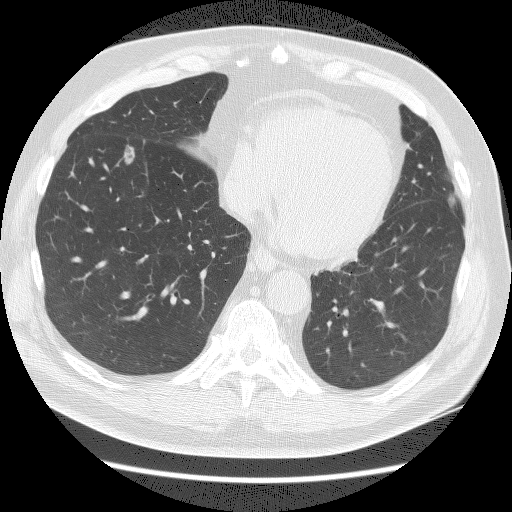
Low-dose screening chest CT, axial slice, baseline annual screen, lung window (W 1500 / L -600 HU), 2.5 mm slice thickness, 140 kVp, slice 109 of 161 in the series. Male participant, aged 65 years at enrolment. Current smoker at enrolment.
• Expert-annotated lung lesion, bounding box <102,134,151,173> (left, top, right, bottom; pixels).
• The screening reader recorded 3 non-calcified nodules or masses ≥4 mm on this exam (right lower lobe, right middle lobe, left upper lobe); which of them this box marks is not recorded.
• Lung cancer was diagnosed 132 days after this screen: adenocarcinoma, NOS, right lower lobe, poorly differentiated (G3), stage IA (AJCC 6th edition), 10 mm at pathology.